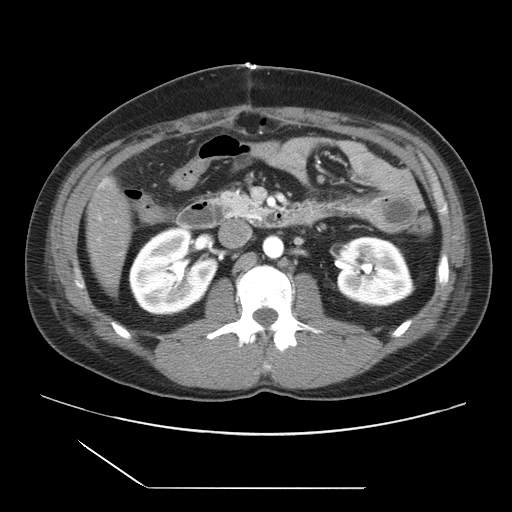
Contrast-enhanced abdominal CT, one axial slice; position 5 of 39 along the scan axis; 120 kVp; intravenous contrast given; soft-tissue window (W 400 / L 40 HU); 5 mm slice thickness; 512 × 512 image matrix. Male patient, age 39 years. From the clinical record (not read from this slice): diagnosis: colorectal cancer liver metastases, imaged before liver resection; multiple liver metastases: yes; largest metastasis: 1.3 cm.
Annotated regions visible in this slice (expert manual segmentation):
- liver: box from (x=88, y=181) to (x=131, y=293) px